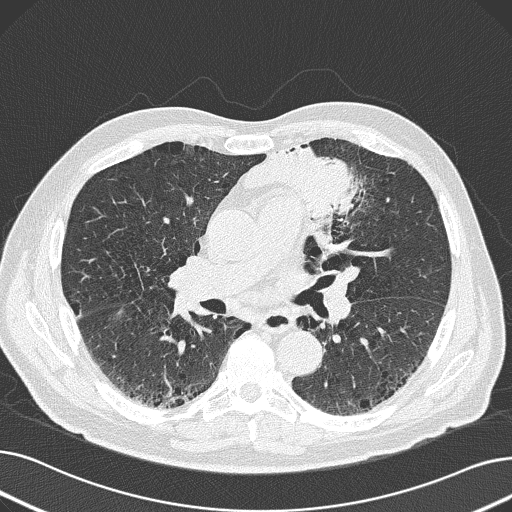
Chest CT (low-dose screening protocol), one axial image. First (baseline) screen. Lung window (W 1500 / L -600 HU). 2 mm slice thickness. 512 × 512 image matrix, field of view 370 × 370 mm. Male participant, aged 69 years at enrolment. Former smoker at enrolment.
• Expert-annotated lung lesion, bounding box [x1, y1, x2, y2] px = [240, 127, 387, 248].
• Reader record for this screening exam (exam-level; its link to the box is not recorded): non-calcified nodule or mass ≥4 mm, left upper lobe, 6 × 10 mm, spiculated (stellate) margins, soft tissue attenuation.
• Later outcome: lung cancer diagnosed 20 days after this screen — non-small cell carcinoma, left upper lobe, poorly differentiated (G3), stage IB (AJCC 6th edition), 100 mm at pathology.